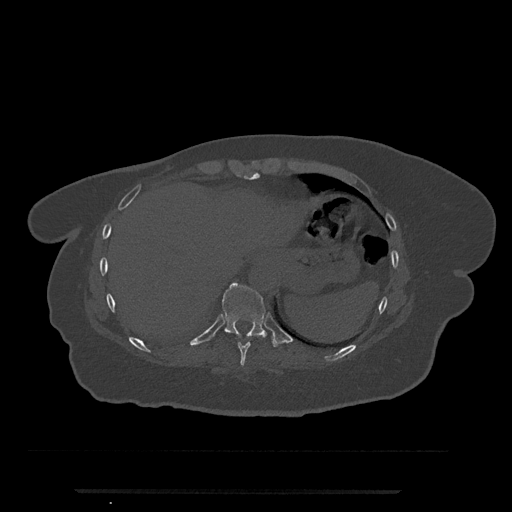
CT including the spine, one axial slice; position 309 of 797 along the scan axis; 120 kVp; bone window (W 1800 / L 400 HU); 0.5 mm slice thickness; 512 × 512 image matrix. Female patient, age 51 years. From the clinical record (not read from this slice): primary cancer: neuro; vertebrae with lytic lesions (as recorded): T8.
Structures marked on this image (semi-automatically segmented with operator editing):
- T10 vertebra: bounding box <222,282,277,347> (left, top, right, bottom; pixels)
- T9 vertebra: <238,342,251,367>